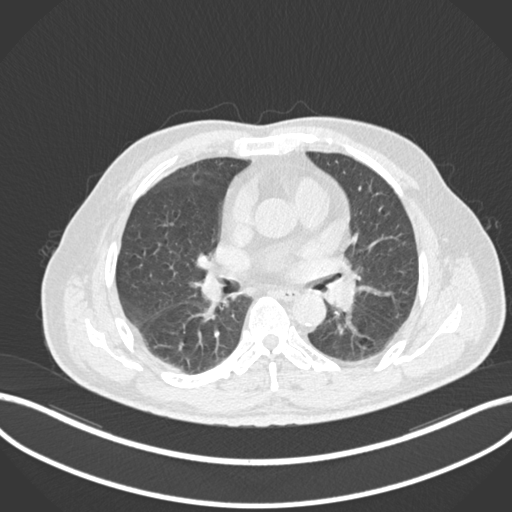
Chest CT, one axial slice; position 73 of 161 along the scan axis; reconstruction kernel B30f; 120 kVp; lung window (W 1500 / L -600 HU); 512 × 512 image matrix, field of view 400 × 400 mm. Patient: male, 71 years. Case-level facts recorded for this patient, not image findings: clinical TNM (as recorded): T1b N0 M0.
Structures marked on this image (bounding box drawn by a radiologist):
- lung tumour (recorded histology: squamous cell carcinoma): bounding box <322,276,362,313> (left, top, right, bottom; pixels)